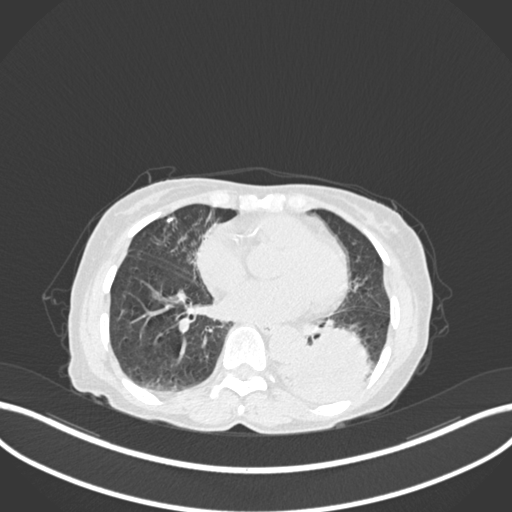
Chest CT, one axial slice. Slice 53 of 233 in the series (ordered by position). Reconstruction kernel B30f. Lung window (W 1500 / L -600 HU). 1 mm slice thickness. 512 × 512 image matrix, field of view 400 × 400 mm. Female patient, age 78 years. From the clinical record (not read from this slice): clinical TNM (as recorded): T3 N0 M1.
Outlined on this slice (bounding box drawn by a radiologist):
- lung tumour (recorded histology: squamous cell carcinoma): box from (x=281, y=323) to (x=373, y=414) px